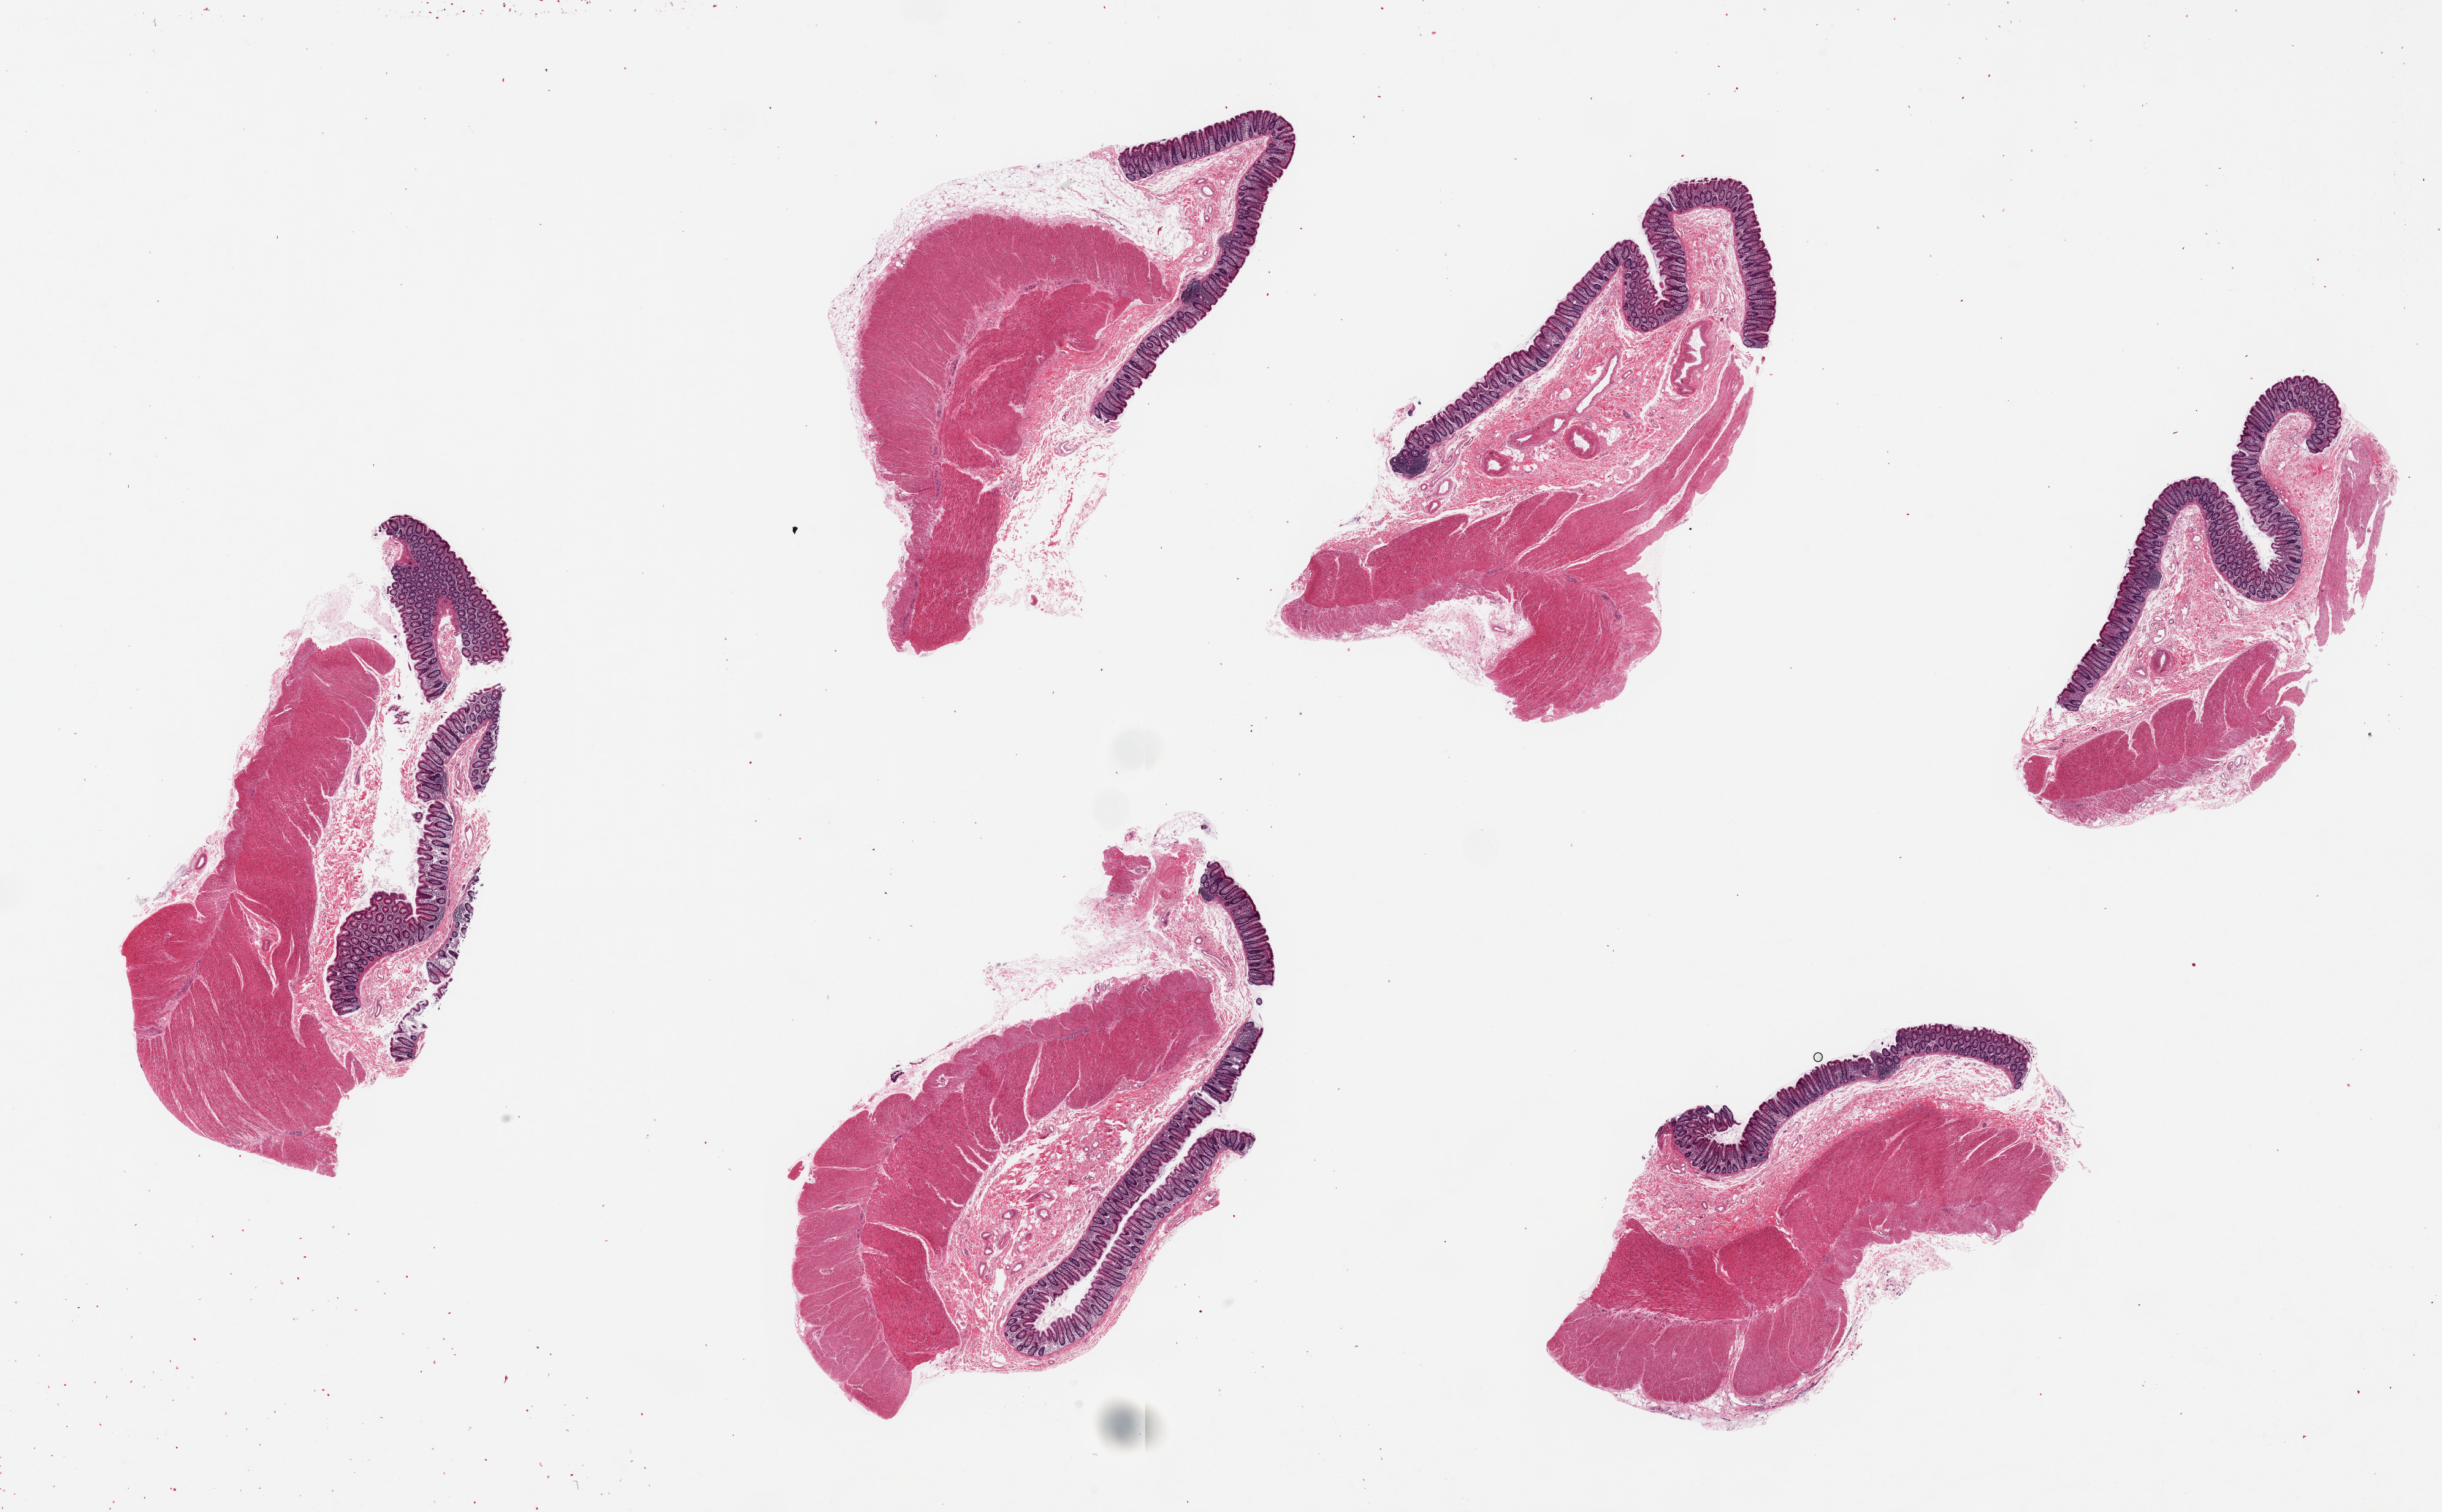
H&E whole-slide image, low-resolution overview of the scanned area, about 31.5 x 19.5 mm (from a 20x scan). PAXgene-fixed, paraffin-embedded tissue. Section of transverse colon (target tissue). Donor tissue sample. Donor sex: female.
- review note (as recorded): 6 pieces, up to 8x4mm; good mucosa and muscularis on all